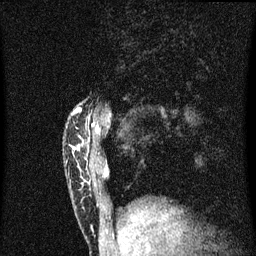
Breast MRI (dynamic contrast-enhanced), one sagittal slice; position 12 of 60 along the scan axis; dynamic contrast-enhanced series, image 2 of 3 at this slice position (ordered by acquisition); 1.5 T; TE 4.2 ms, TR 8.4 ms; 256 × 256 image matrix, field of view 200 × 200 mm. Patient: female, 40 years.
Structures marked on this image (semi-automatically segmented with operator editing):
- analysis volume of interest (the breast-tissue region the enhancement analysis was run in; not a lesion): bounding box <73,106,102,203> (left, top, right, bottom; pixels)
- tumour enhancement mask (voxels above the 70 % enhancement threshold inside the analysis volume of interest): <73,108,82,149>